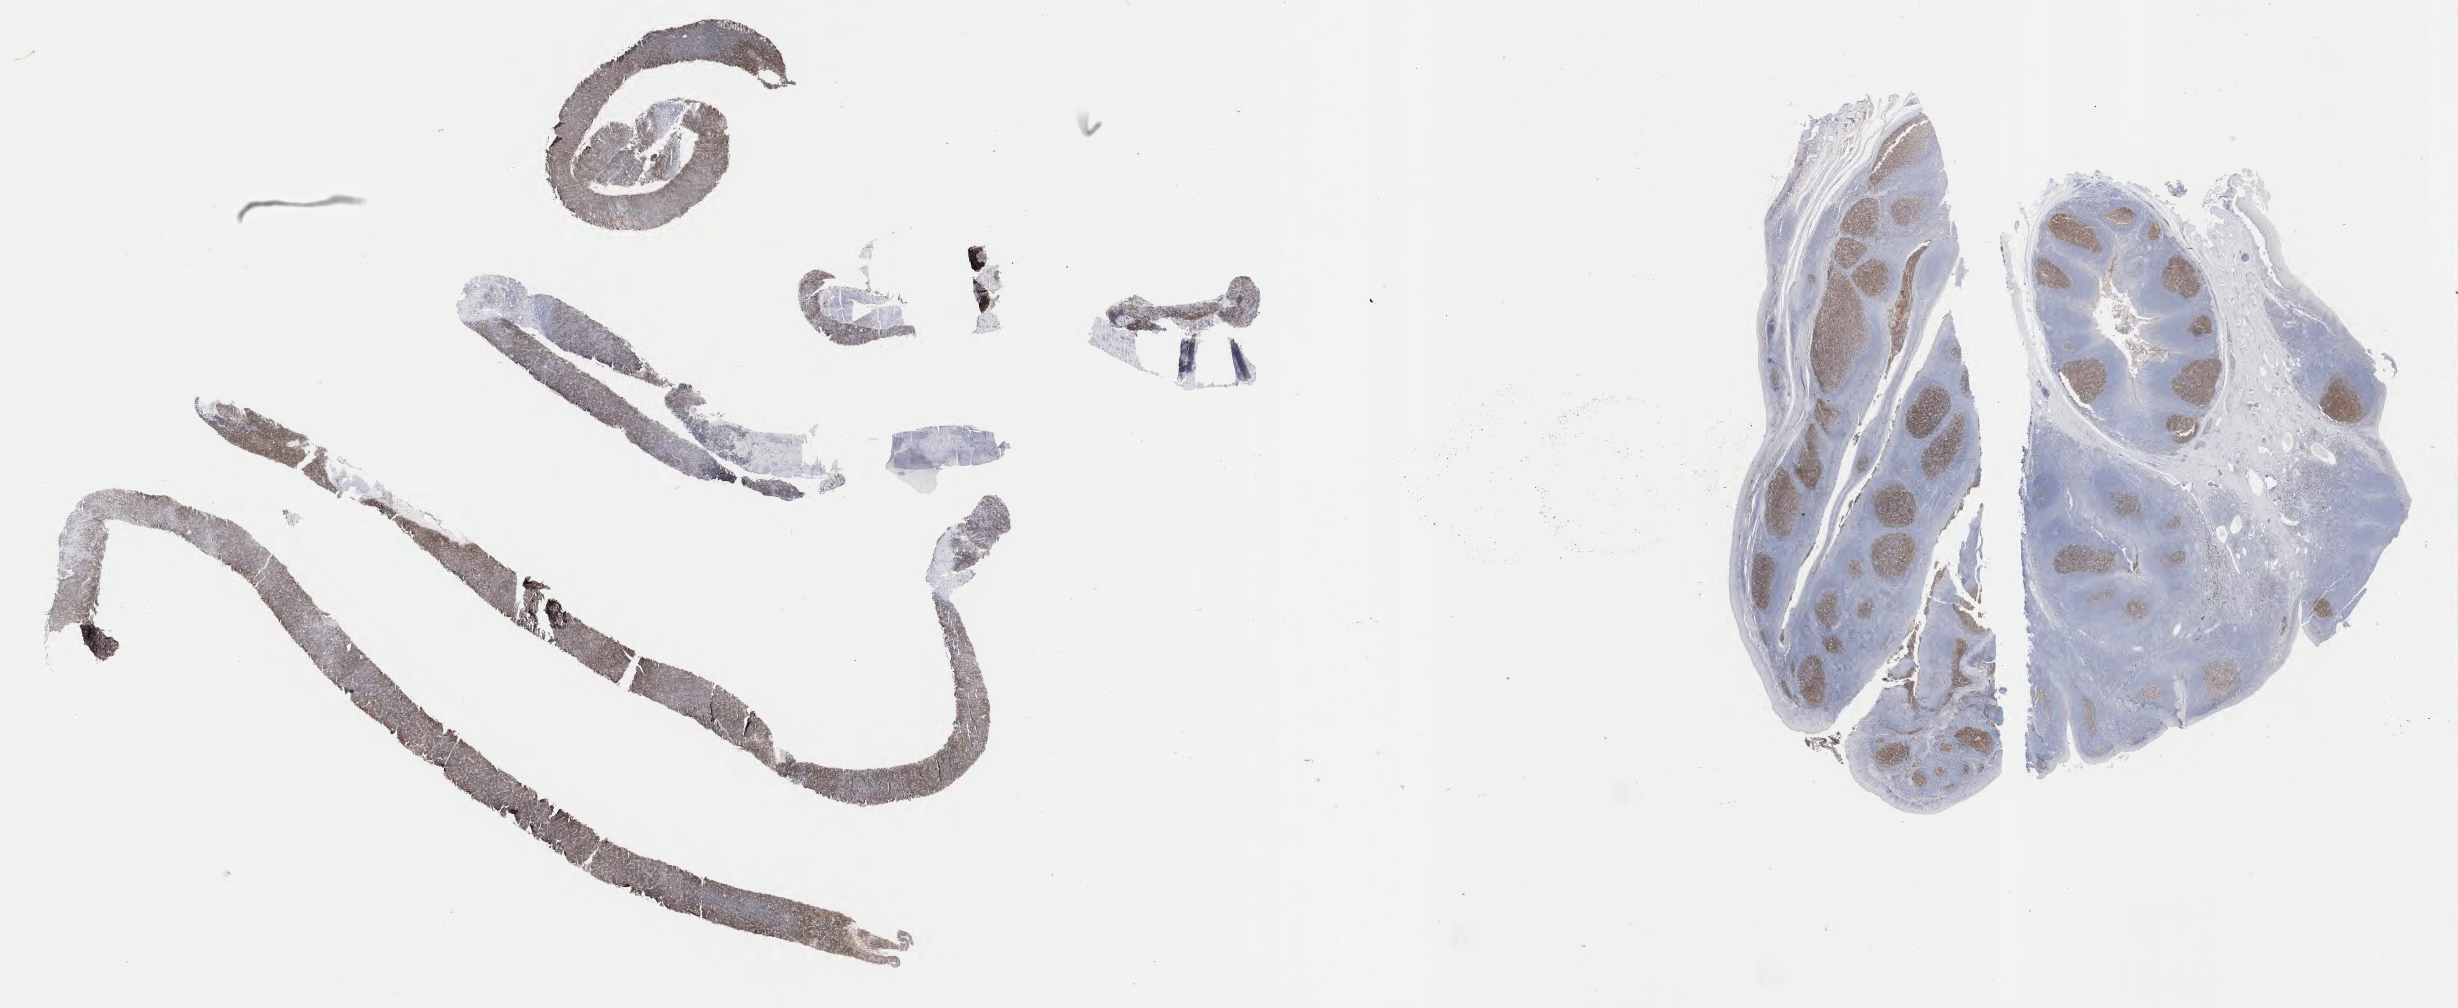
IHC for CD10, whole-slide image, low-resolution overview of the scanned area, about 39.8 x 16.3 mm, tumor tissue. Patient male; age 45 years.
Diagnosis: Burkitt lymphoma, NOS.